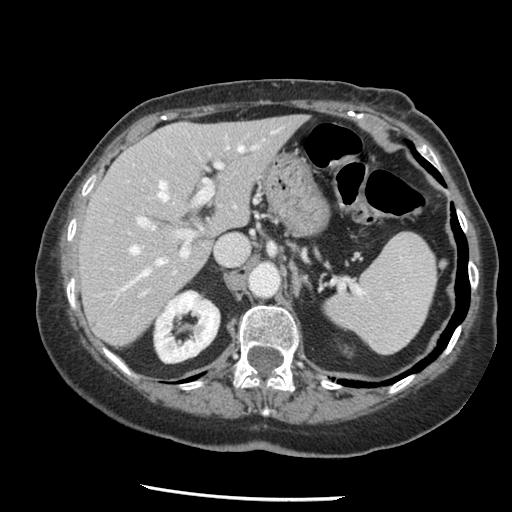
Contrast-enhanced abdominal CT, one axial slice; slice 87 of 148 in the series (ordered by position); 120 kVp; soft-tissue window (W 400 / L 40 HU); 2.5 mm slice thickness; 512 × 512 image matrix, field of view 330 × 330 mm. Female patient, age 85 years. Case-level facts recorded for this patient, not image findings: diagnosis: colorectal cancer liver metastases, imaged before liver resection; multiple liver metastases: no.
Outlined on this slice (manually delineated by an expert):
- hepatic veins: box from (x=123, y=147) to (x=243, y=289) px
- liver: (x=80, y=118)–(x=303, y=346)
- planned liver remnant (the part of the liver to remain after resection): (x=80, y=118)–(x=303, y=346)
- portal vein (with intrahepatic branches): (x=138, y=140)–(x=230, y=256)